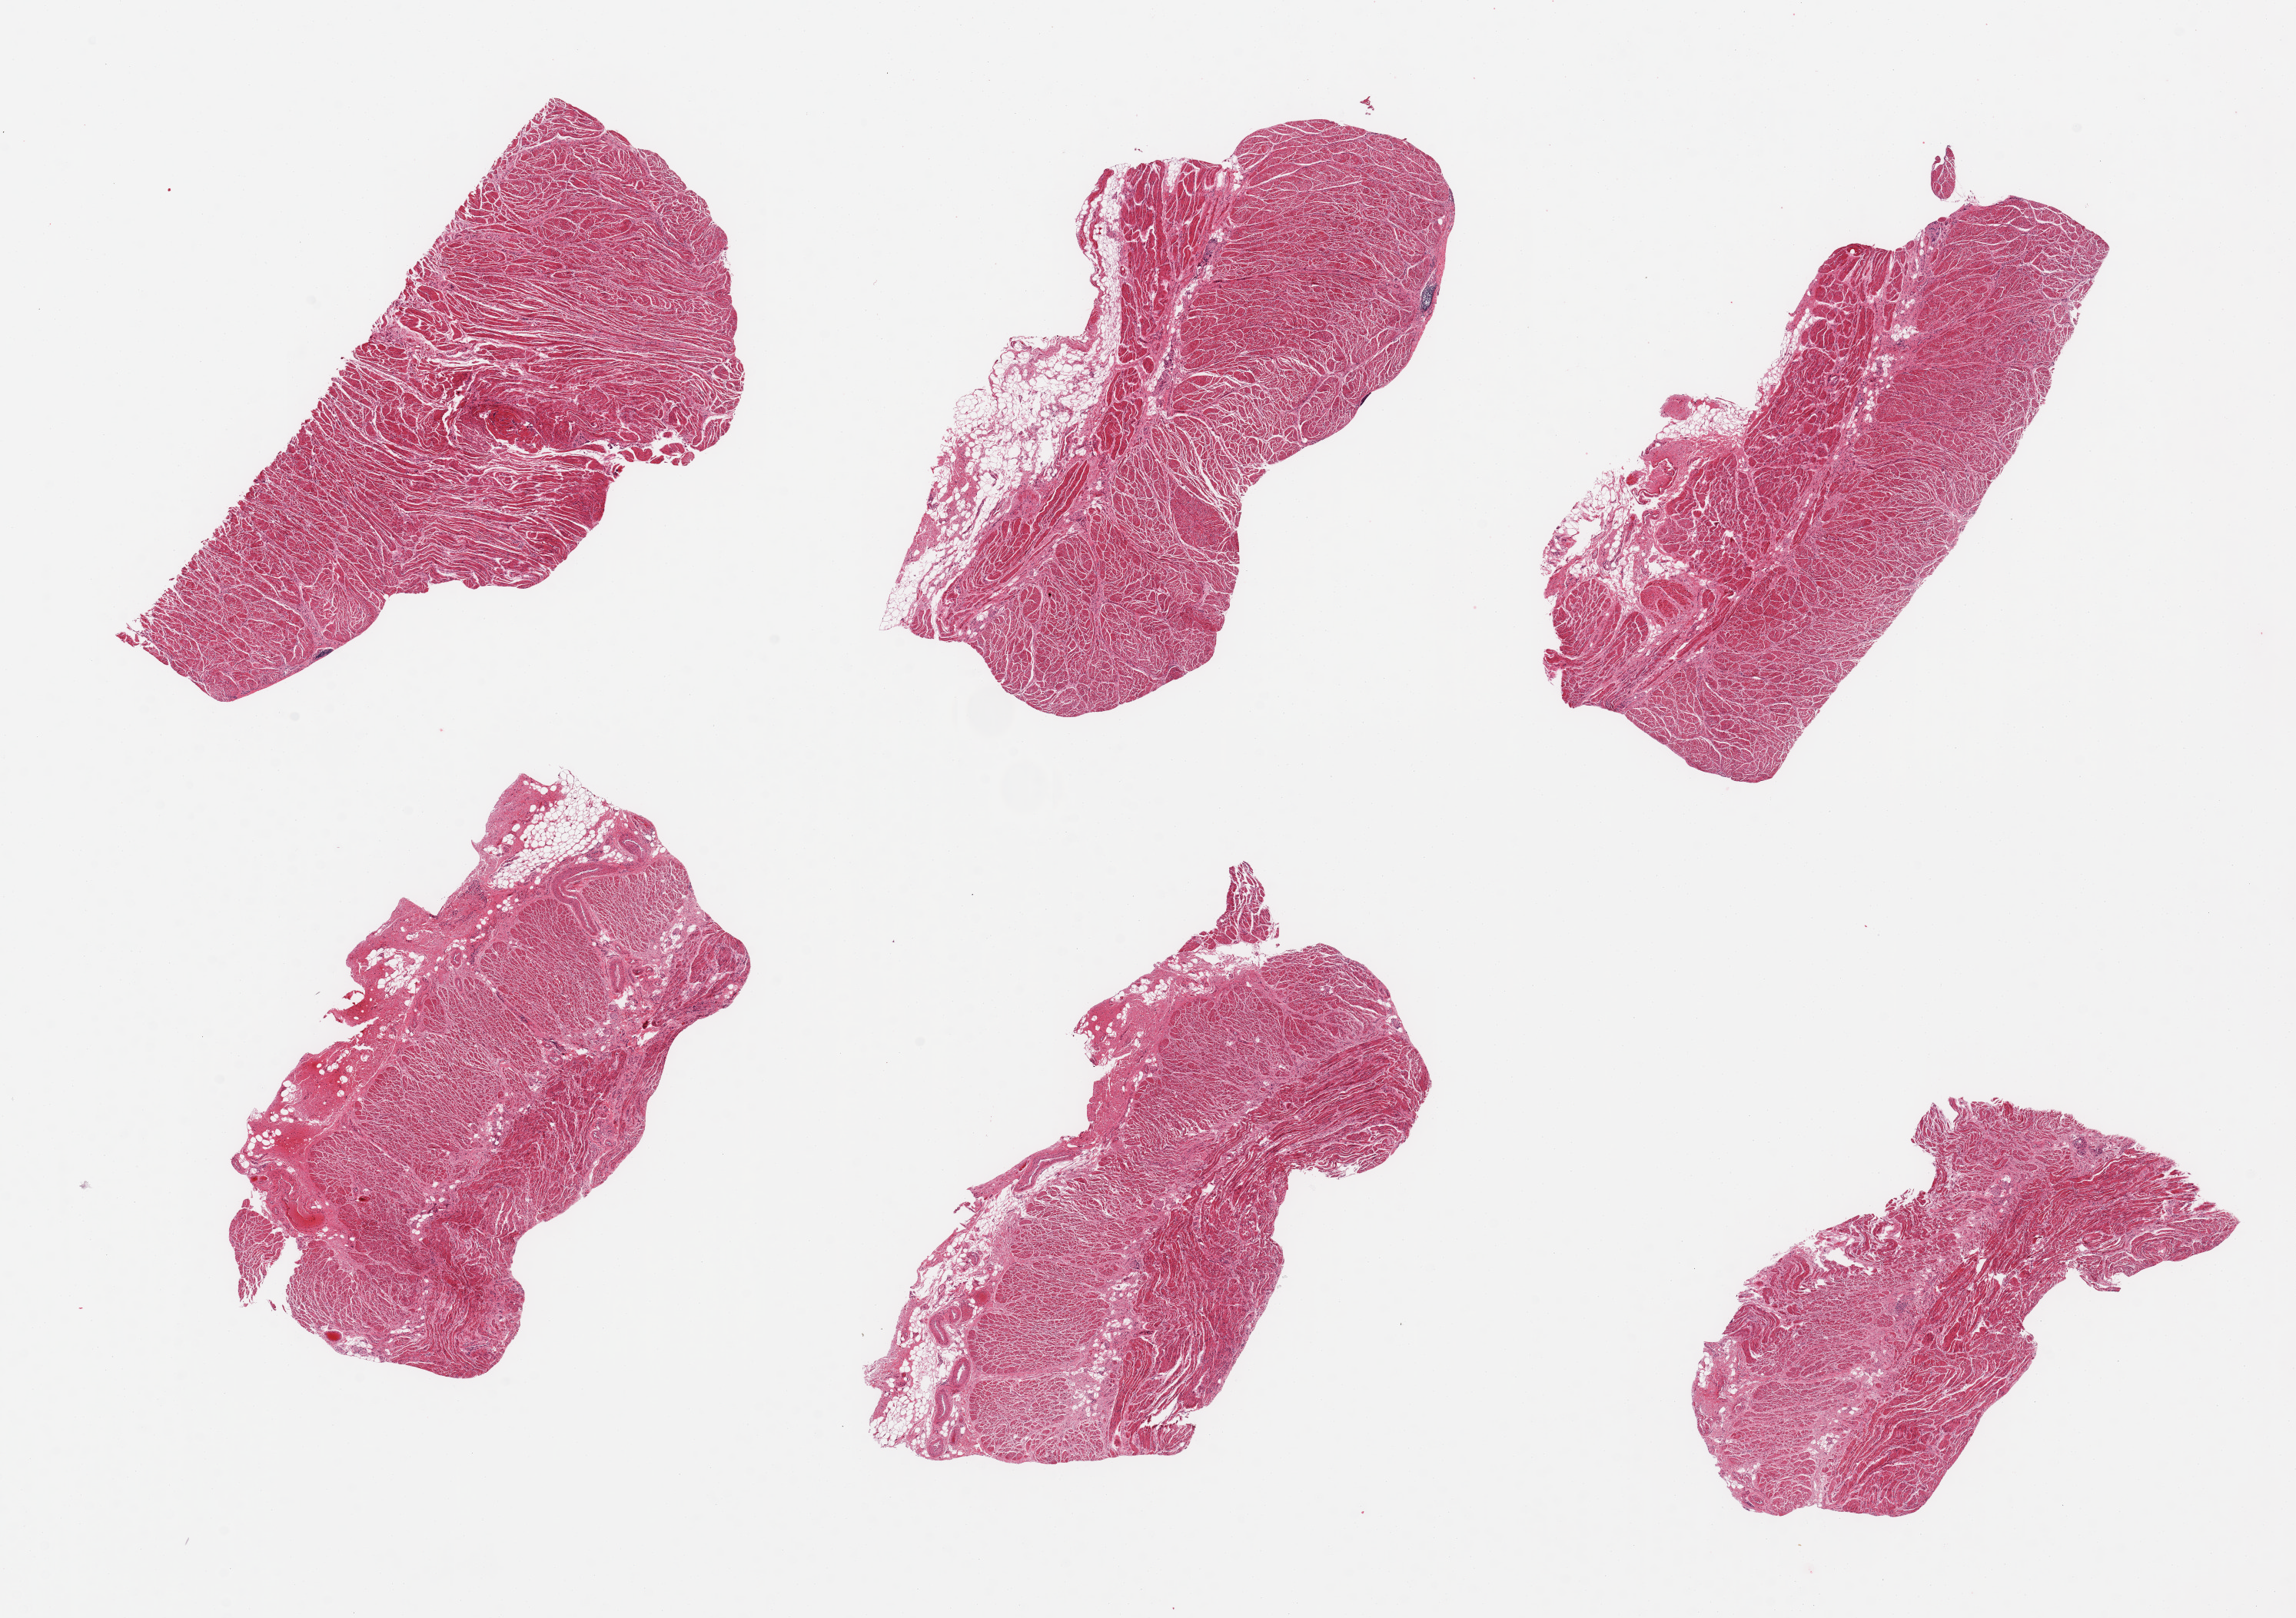
Digitized haematoxylin and eosin-stained section, brightfield — a low-resolution overview of the entire scanned area, about 23.6 x 16.6 mm (slide scanned at 20x), PAXgene-fixed paraffin-embedded (PFPE) section, section of gastroesophageal junction (target tissue), donor tissue sample. Donor sex: male.
Reviewer comment on this tissue sample: 6 pieces, confirmed target muscularis.